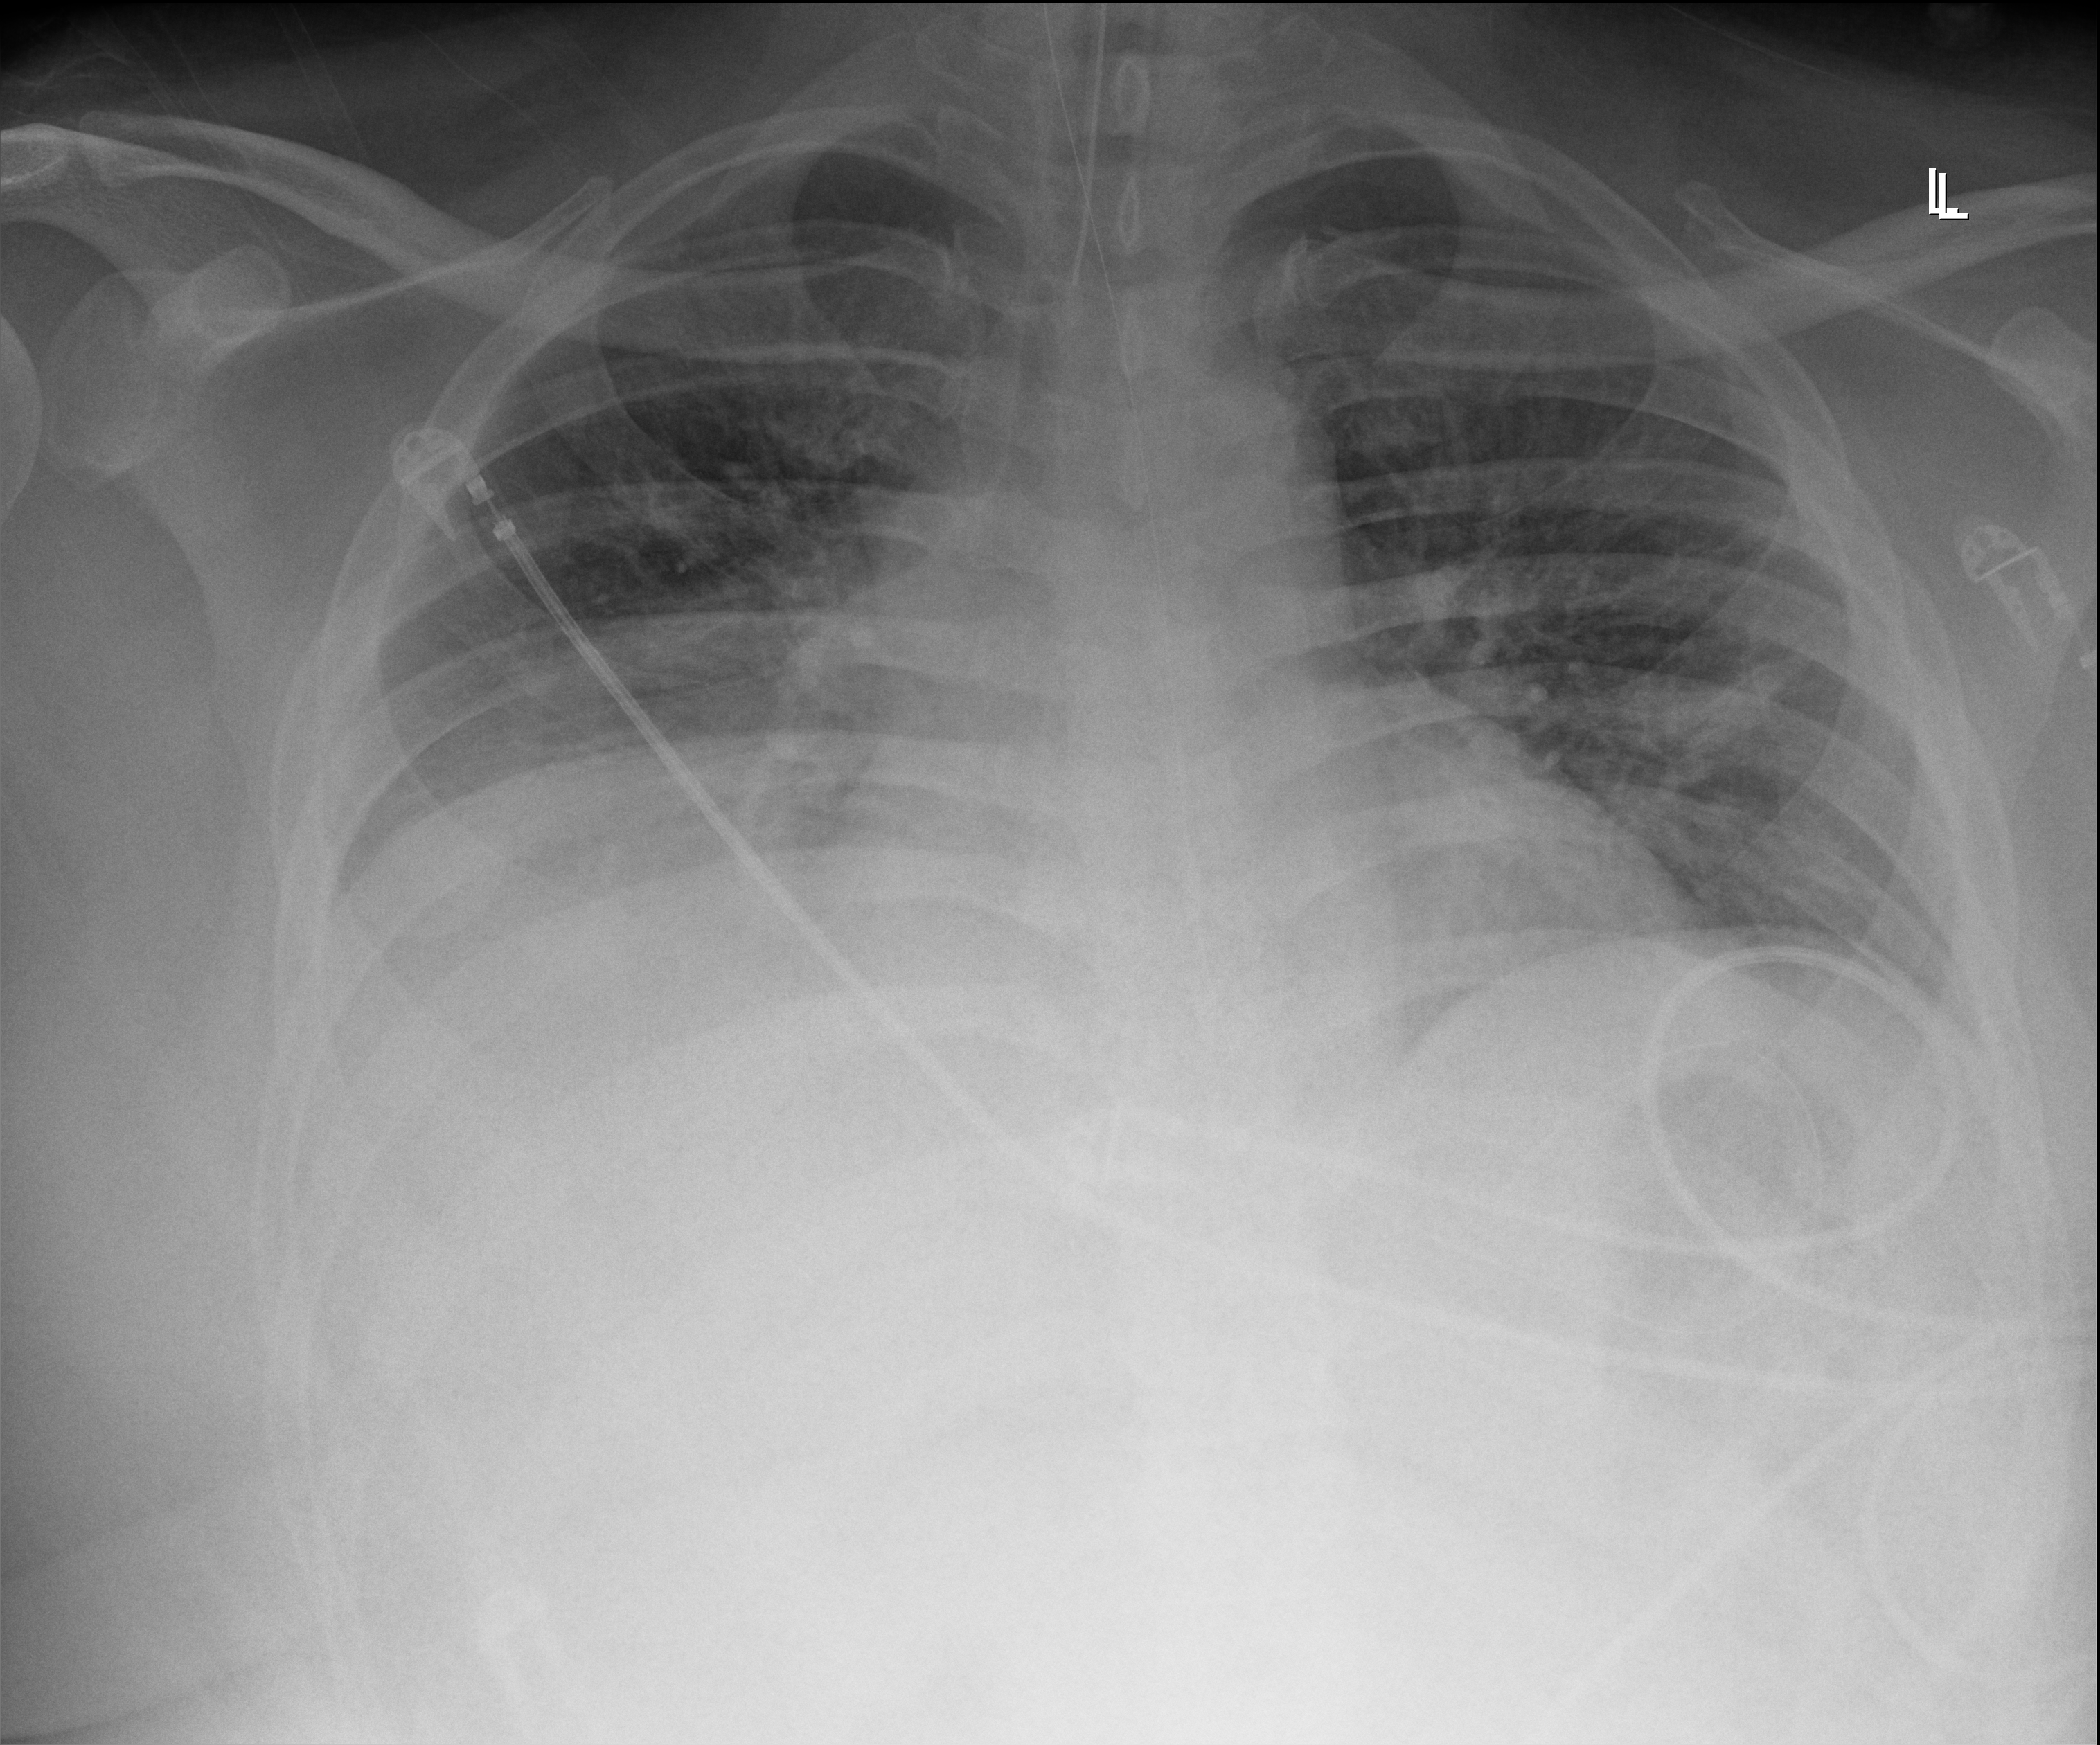
Chest X-ray (portable); anteroposterior (AP) projection. Male patient hospitalised with COVID-19, age 18–59 years.
Admission-level facts for this patient (not findings on this image; timing relative to this image not recorded): admitted to intensive care during this hospital stay: yes; smoking status (admission record): never.